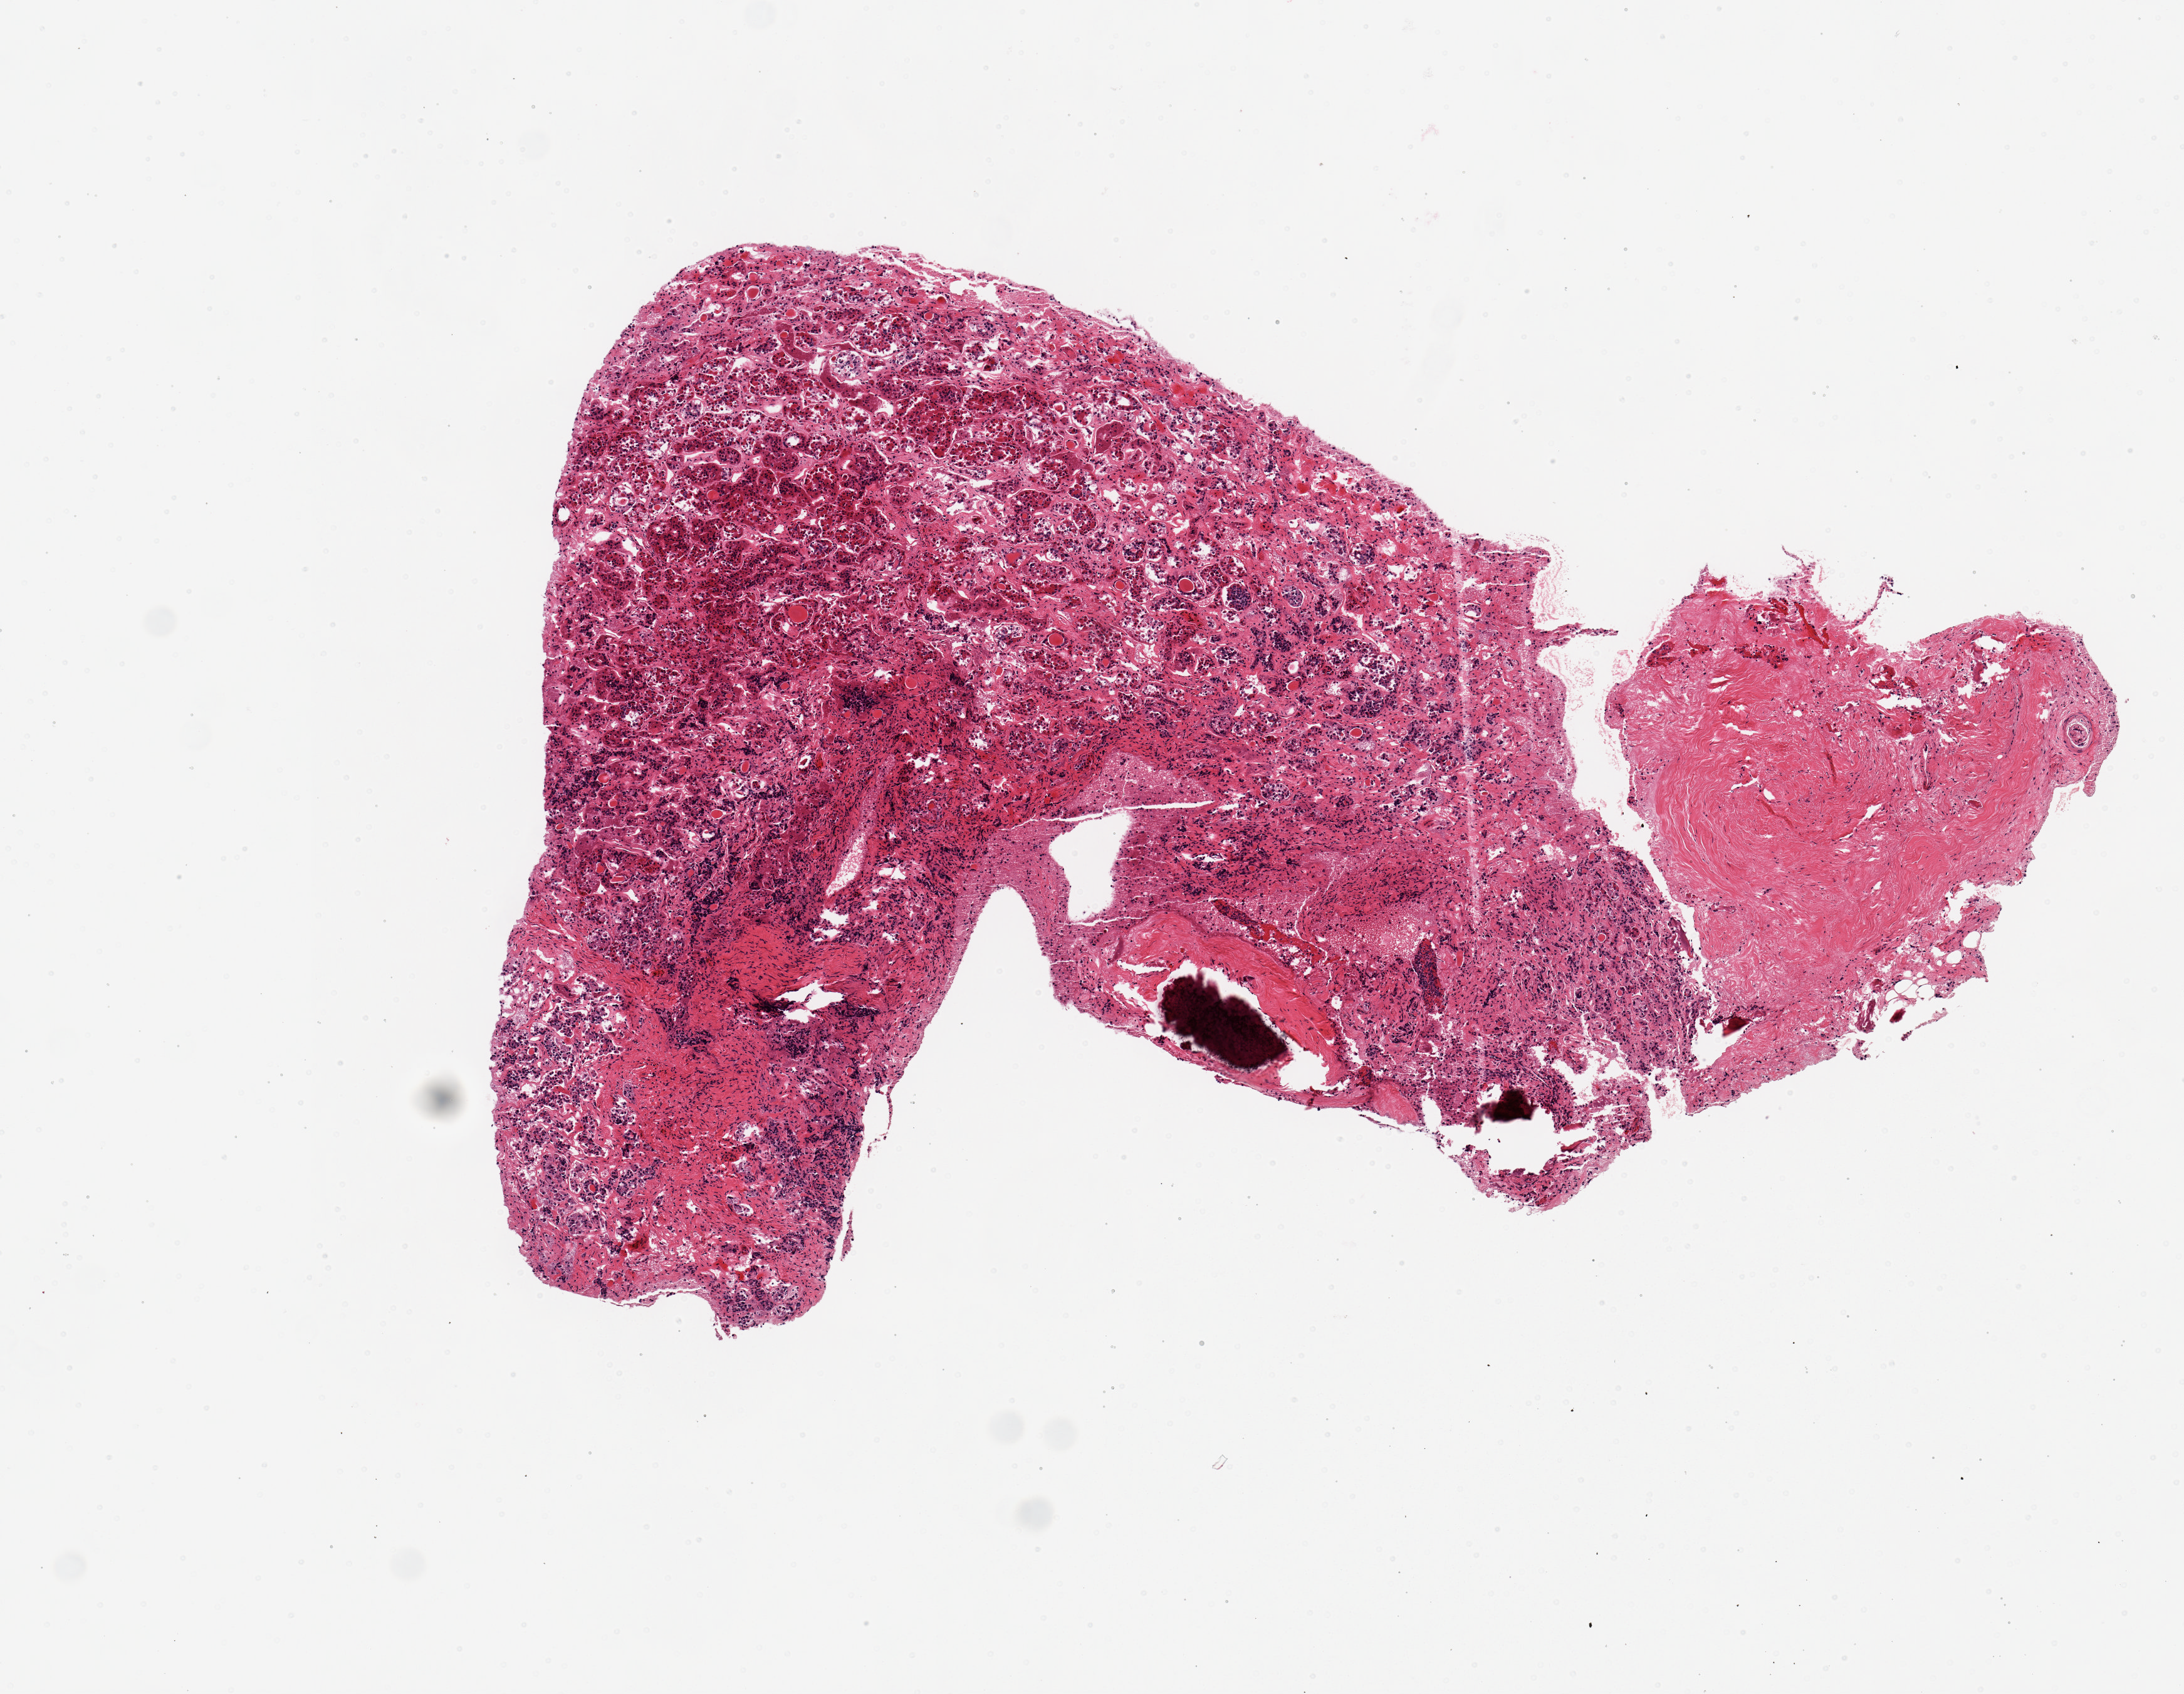
Hematoxylin and eosin (H&E) whole-slide image, a low-resolution overview of the entire scanned area, about 6.9 x 5.3 mm. PAXgene-fixed paraffin-embedded (PFPE) section. Section of pituitary (target tissue). Donor tissue sample.
Pathologist's review note for this sample: 1 piece; adenohypophysis and portion of dura.